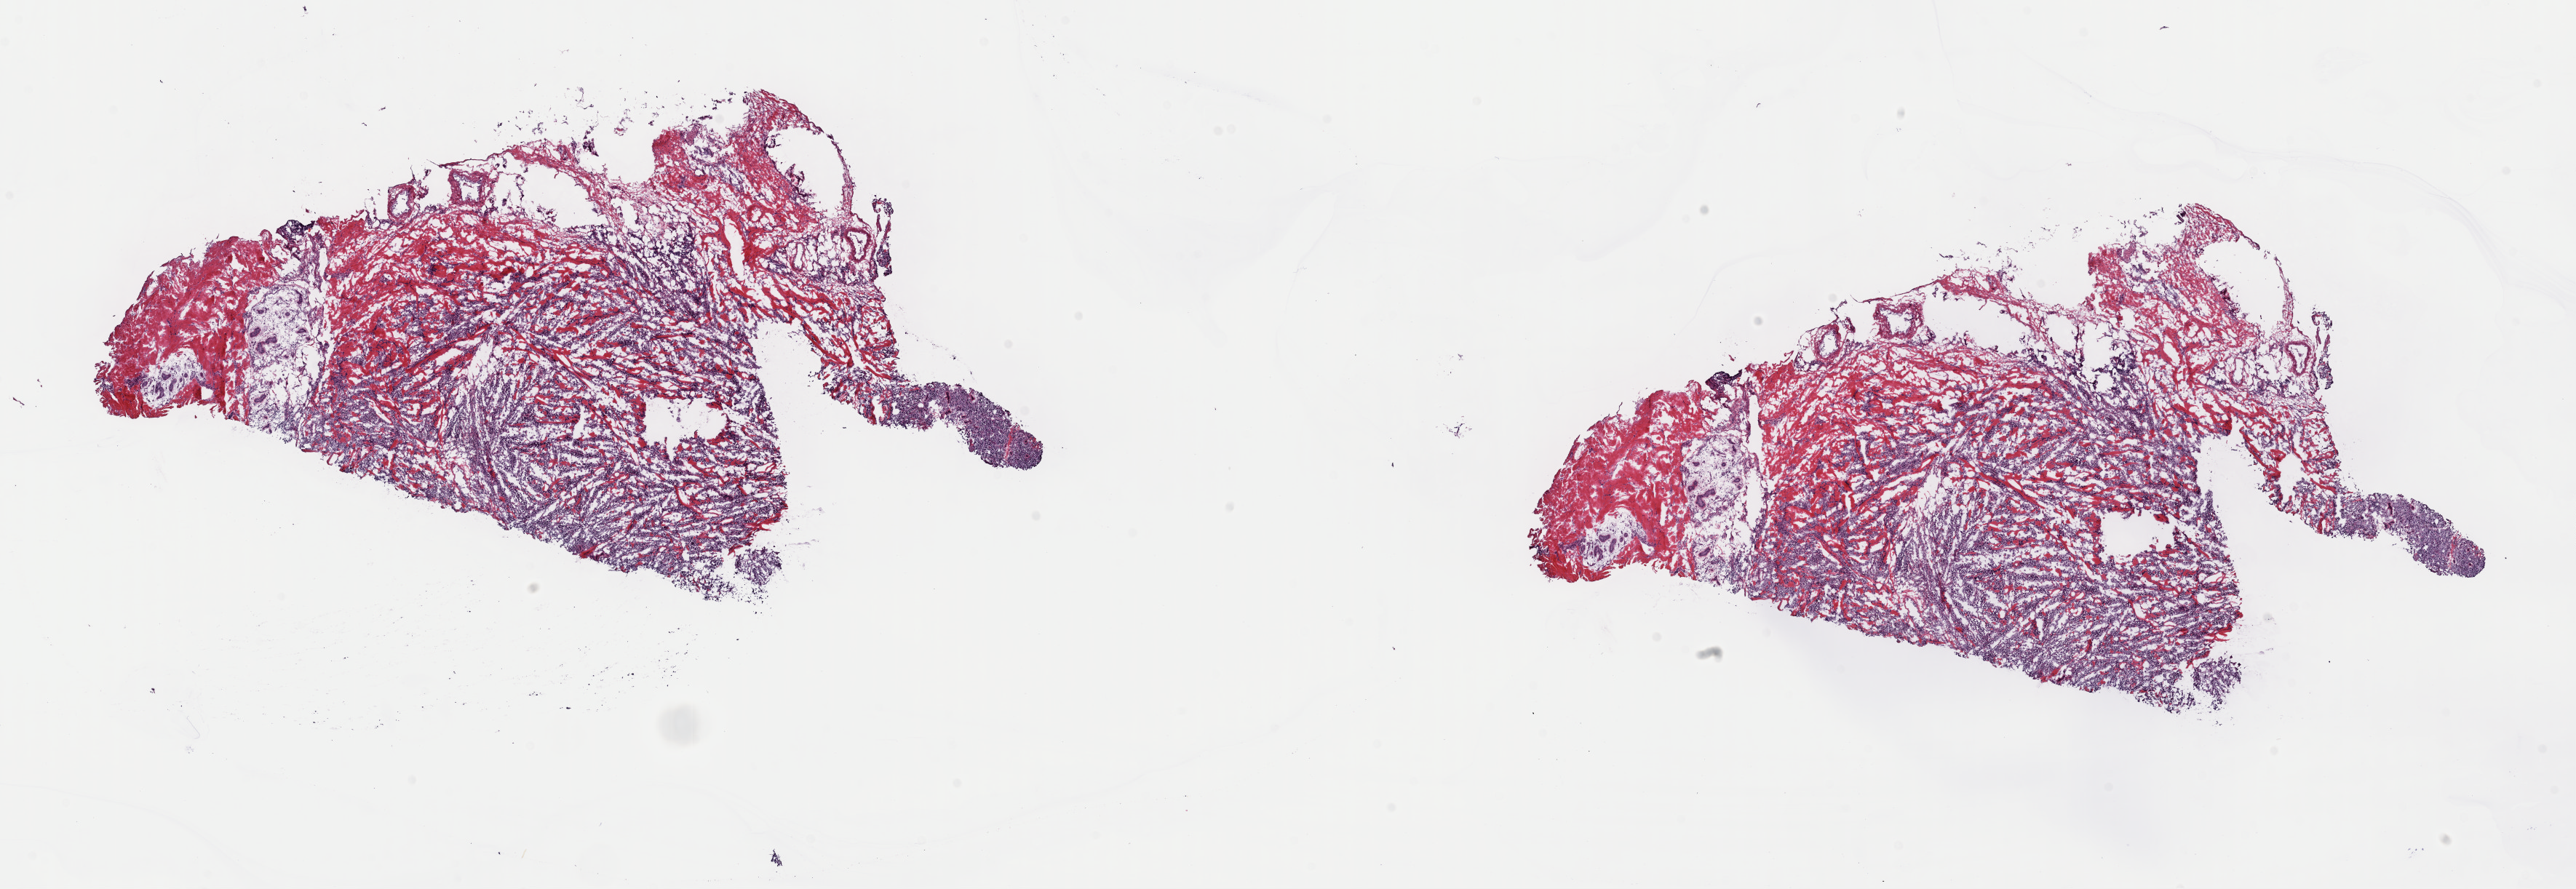
H&E-stained whole-slide image, shown as a low-resolution overview of the whole scanned area (about 28.0 x 9.7 mm, from a 40x scan); frozen section from the top of the tissue portion; sample: primary tumour, skin. Patient: male, age at initial diagnosis 62 years. Composition of this section per pathologist review: tumour cells 80%, tumour nuclei 85%, normal cells 20%, stromal cells 0%, necrosis 0%. Infiltration values recorded for this section: lymphocyte infiltration 0%, monocyte infiltration 0%, neutrophil infiltration 0%.
- histologic diagnosis: Malignant melanoma, NOS
- AJCC pathologic stage: IIC (7th edition)
- TNM: T4b N0 M0